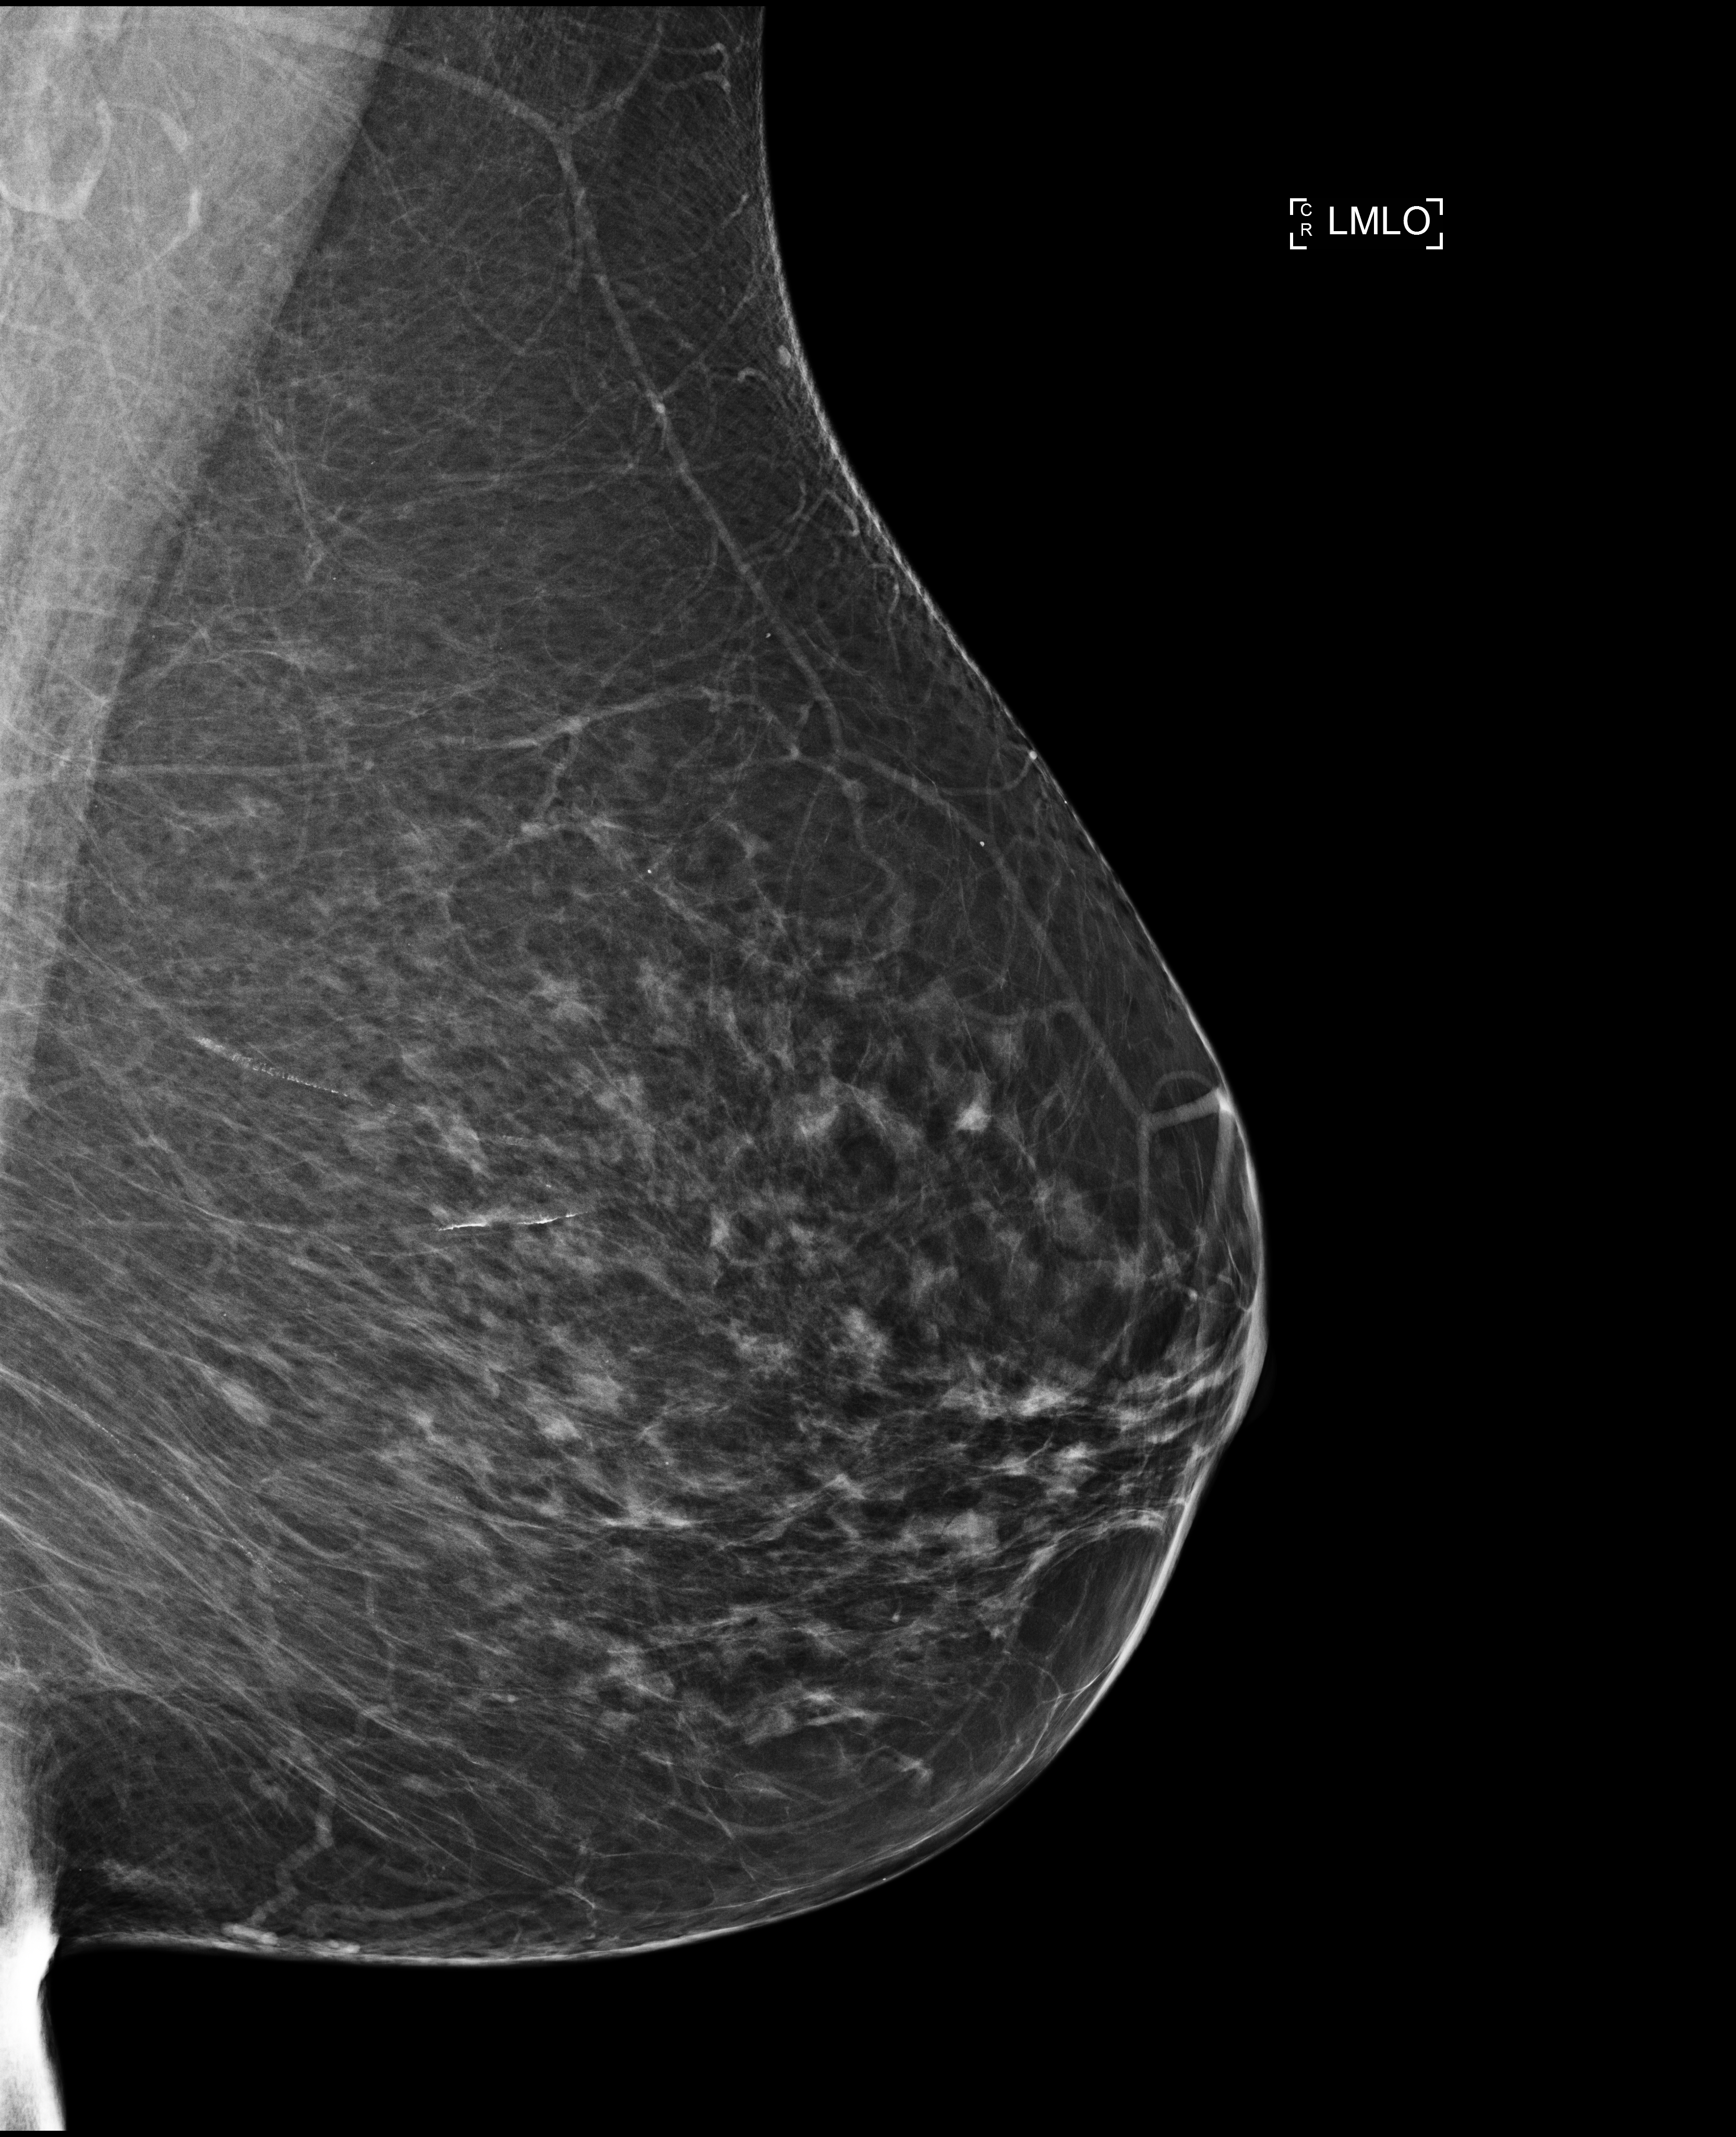
Annual screening mammography examination, compressed breast thickness 71 mm, system: Selenia Dimensions. Female patient, age 74 years.
Image type: full-field digital mammogram. Breast: left. Projection: medio-lateral oblique projection.